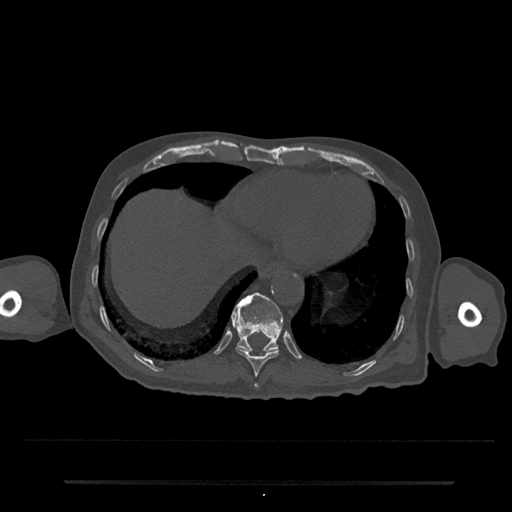
CT including the spine, one axial slice. Position 289 of 797 along the scan axis. Reconstruction kernel Br40s/3. 120 kVp. Bone window (W 1800 / L 400 HU). 512 × 512 image matrix. Male patient, age 74 years. From the clinical record (not read from this slice): primary cancer: prostate.
Structures marked on this image (semi-automatic segmentation, software-assisted and operator-edited):
- T10 vertebra: bounding box [x1, y1, x2, y2] px = [236, 336, 279, 376]
- T11 vertebra: [231, 292, 283, 353]
- T9 vertebra: [254, 383, 258, 388]